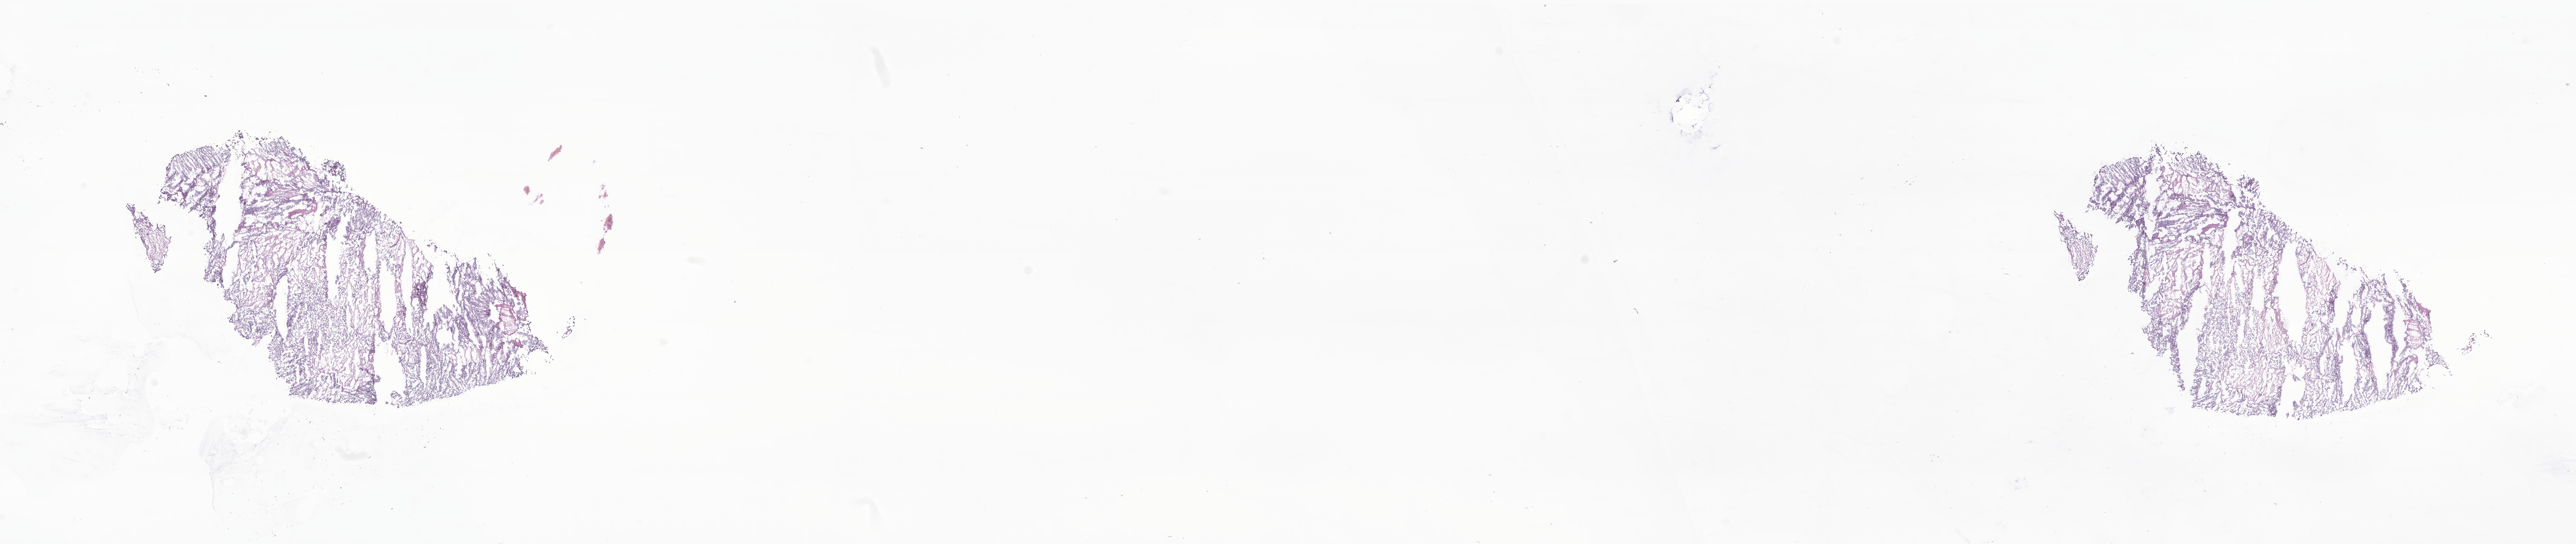
Whole-slide image, H&E stain of tumor tissue from the cerebellum, a low-resolution overview of the entire scanned area, about 37.1 x 7.8 mm. Frozen section. Female patient, age 115 months (9 years 7 months).
- diagnosis: Medulloblastoma, NOS